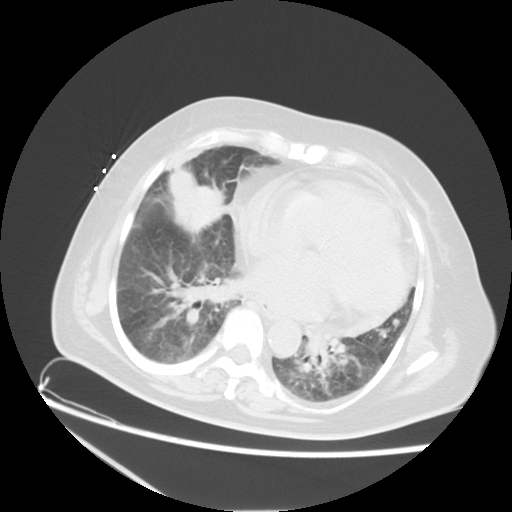
Chest CT, one axial slice; position 7 of 22 along the scan axis; reconstruction kernel STANDARD; 120 kVp; lung window (W 1500 / L -600 HU); 5 mm slice thickness; 512 × 512 image matrix, field of view 350 × 350 mm. Female patient, age 67 years. From the clinical record (not read from this slice): clinical TNM (as recorded): T2a N3 M1a.
Outlined on this slice (rectangle marked by the reading radiologist):
- lung tumour (recorded histology: adenocarcinoma): box from (x=169, y=165) to (x=225, y=236) px